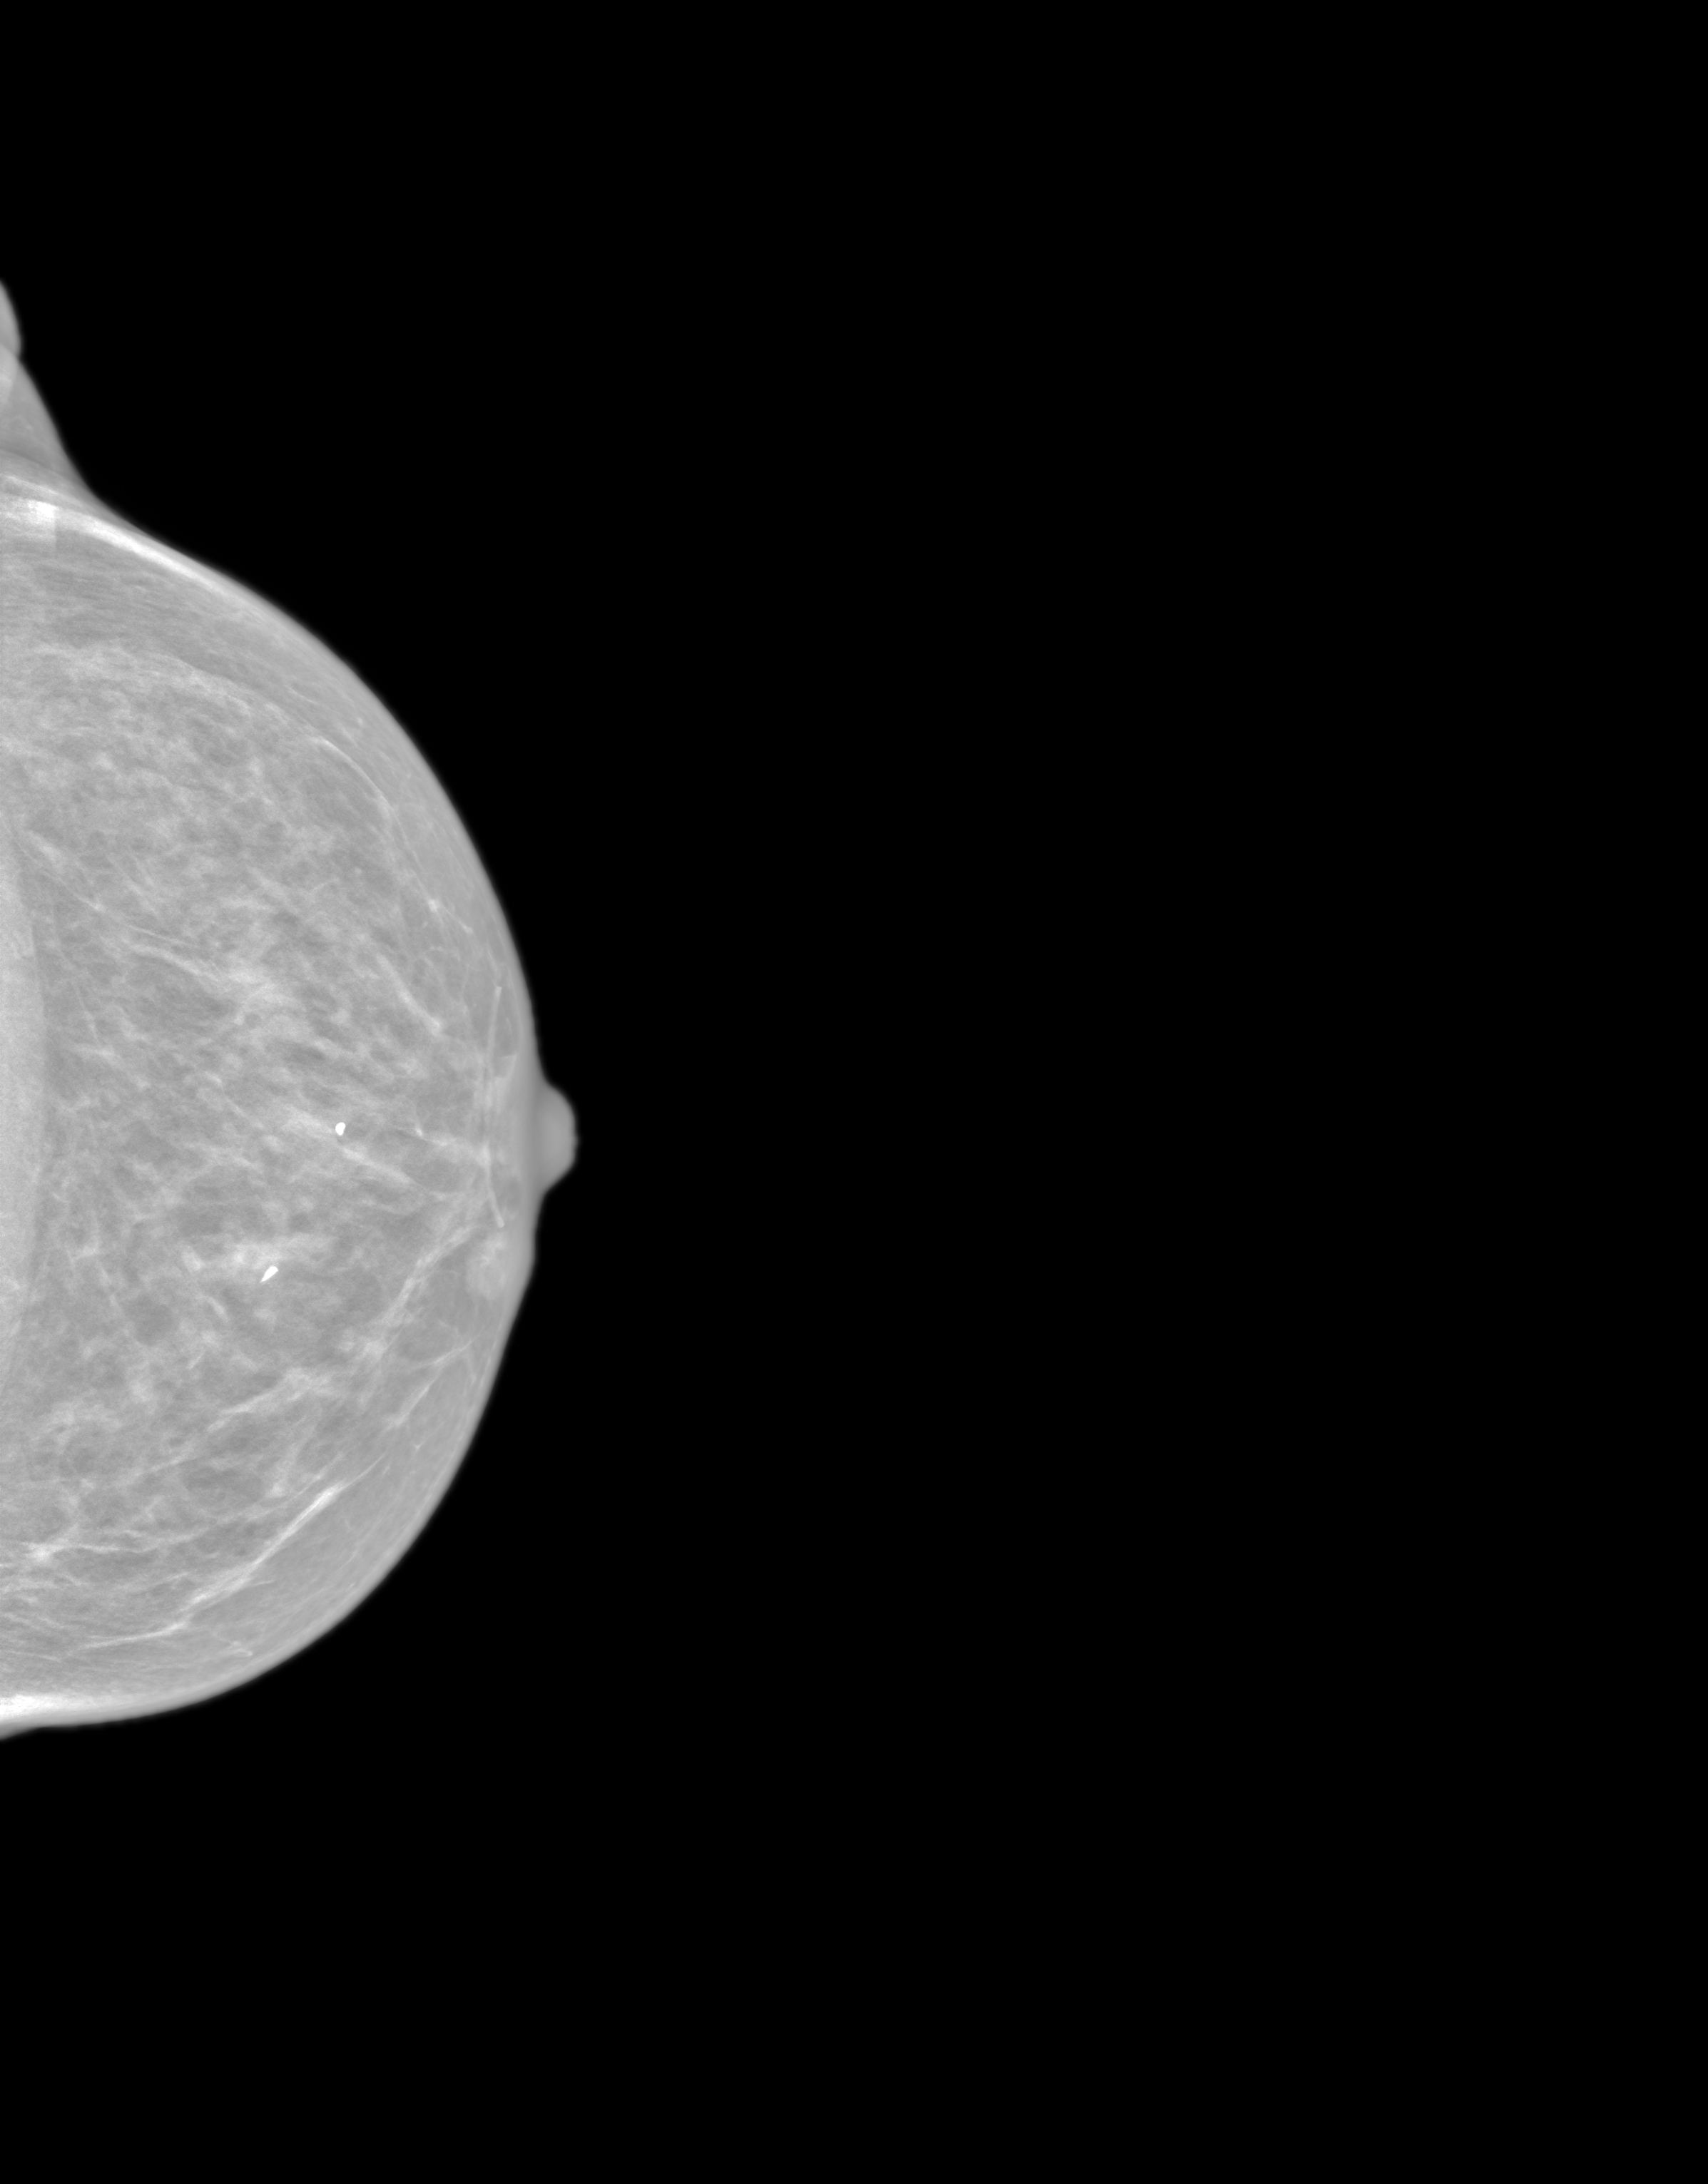
Annual screening mammography examination. Female patient, age 70 years.
Image type: synthesized 2-D view from tomosynthesis. Breast: left. Projection: craniocaudal (CC) view.